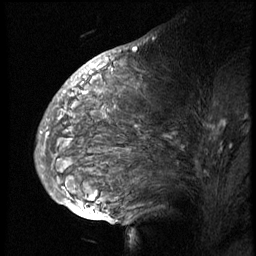
Breast MRI (dynamic contrast-enhanced), one sagittal slice. Slice 35 of 74 in the series (ordered by position). 3 images stored at this slice position (order not interpretable as contrast timing). 1.5 T. TE 4.2 ms, TR 8.9 ms. 2.5 mm slice thickness. 256 × 256 image matrix, field of view 200 × 200 mm. Patient: female, 57 years. Case-level facts recorded for this patient, not image findings: setting: breast cancer imaged before/during neoadjuvant chemotherapy; receptor status: HER2-positive.
Outlined on this slice (semi-automatic segmentation, software-assisted and operator-edited):
- analysis volume of interest (the breast-tissue region the enhancement analysis was run in; not a lesion): bounding box [x1, y1, x2, y2] px = [51, 67, 249, 173]
- tumour enhancement mask (voxels above the 140 % enhancement threshold inside the analysis volume of interest): [94, 67, 138, 127]